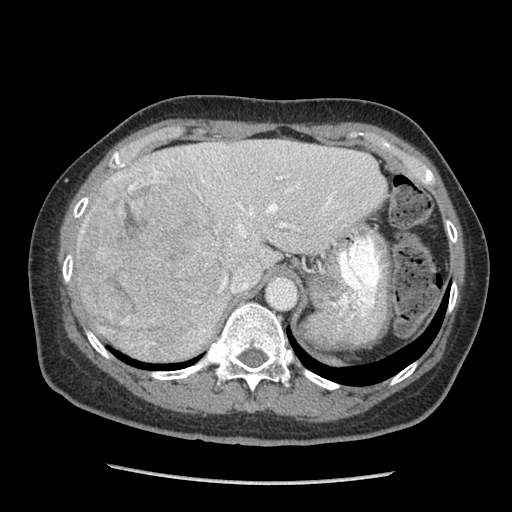
Contrast-enhanced abdominal CT (liver protocol), one axial slice; slice 64 of 105 in the series (ordered by position); 140 kVp; soft-tissue window (W 400 / L 40 HU); 2.5 mm slice thickness; 512 × 512 image matrix. From the clinical record (not read from this slice): diagnosis: hepatocellular carcinoma (patient treated with transarterial chemoembolisation; whether this scan precedes or follows treatment is not stated here); TNM stage (as recorded): Stage-I; Child-Pugh class: A; tumour nodularity: uninodular; tumour size: 11.1 cm.
Annotated regions visible in this slice (semi-automatically segmented with operator editing):
- abdominal aorta: bounding box [x1, y1, x2, y2] px = [268, 277, 296, 308]
- liver parenchyma outside the tumour (the mass and vessels are separate outlines, so this box may not span the whole liver): [76, 140, 386, 360]
- mass: [76, 167, 224, 348]
- liver vessels: [119, 149, 332, 290]